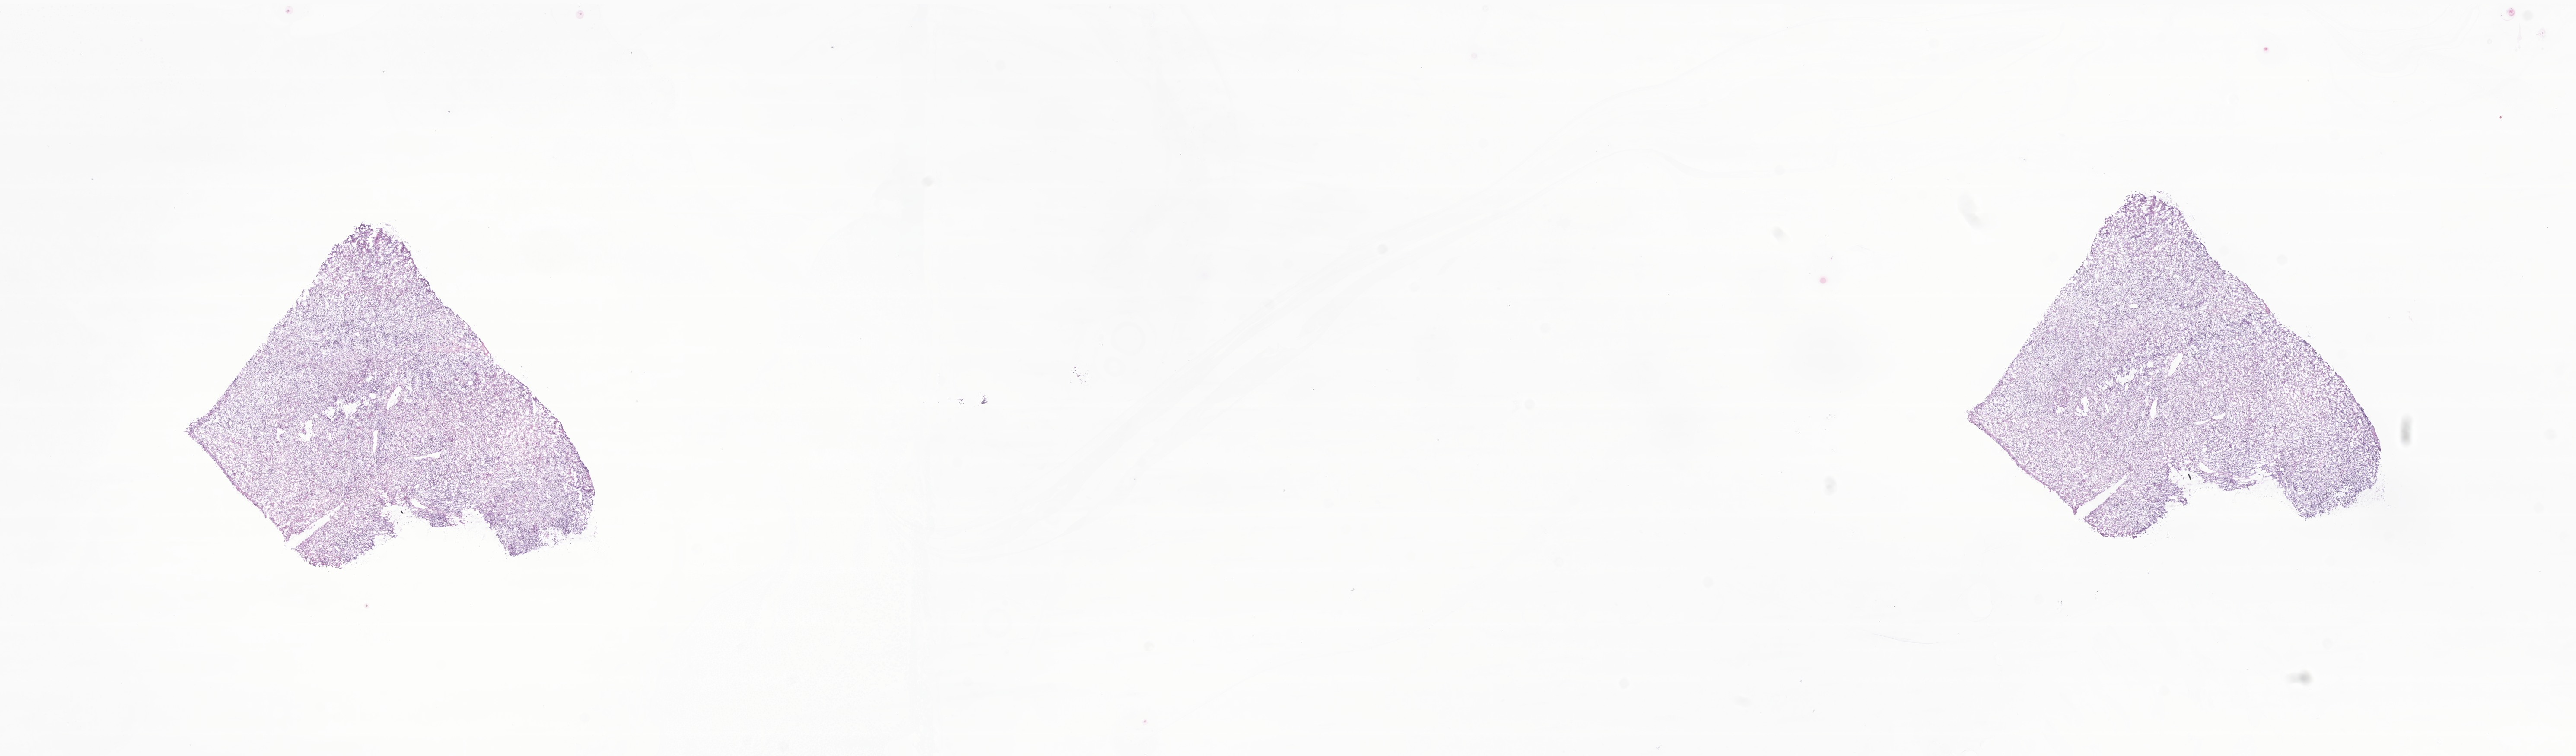
Digitized H&E-stained section of tumor tissue from the testis — a low-resolution overview of the entire scanned area, about 25.1 x 7.4 mm; frozen section (OCT-embedded). Patient male; age 185 months (15 years 5 months).
Diagnosis: Rhabdomyosarcoma, NOS.